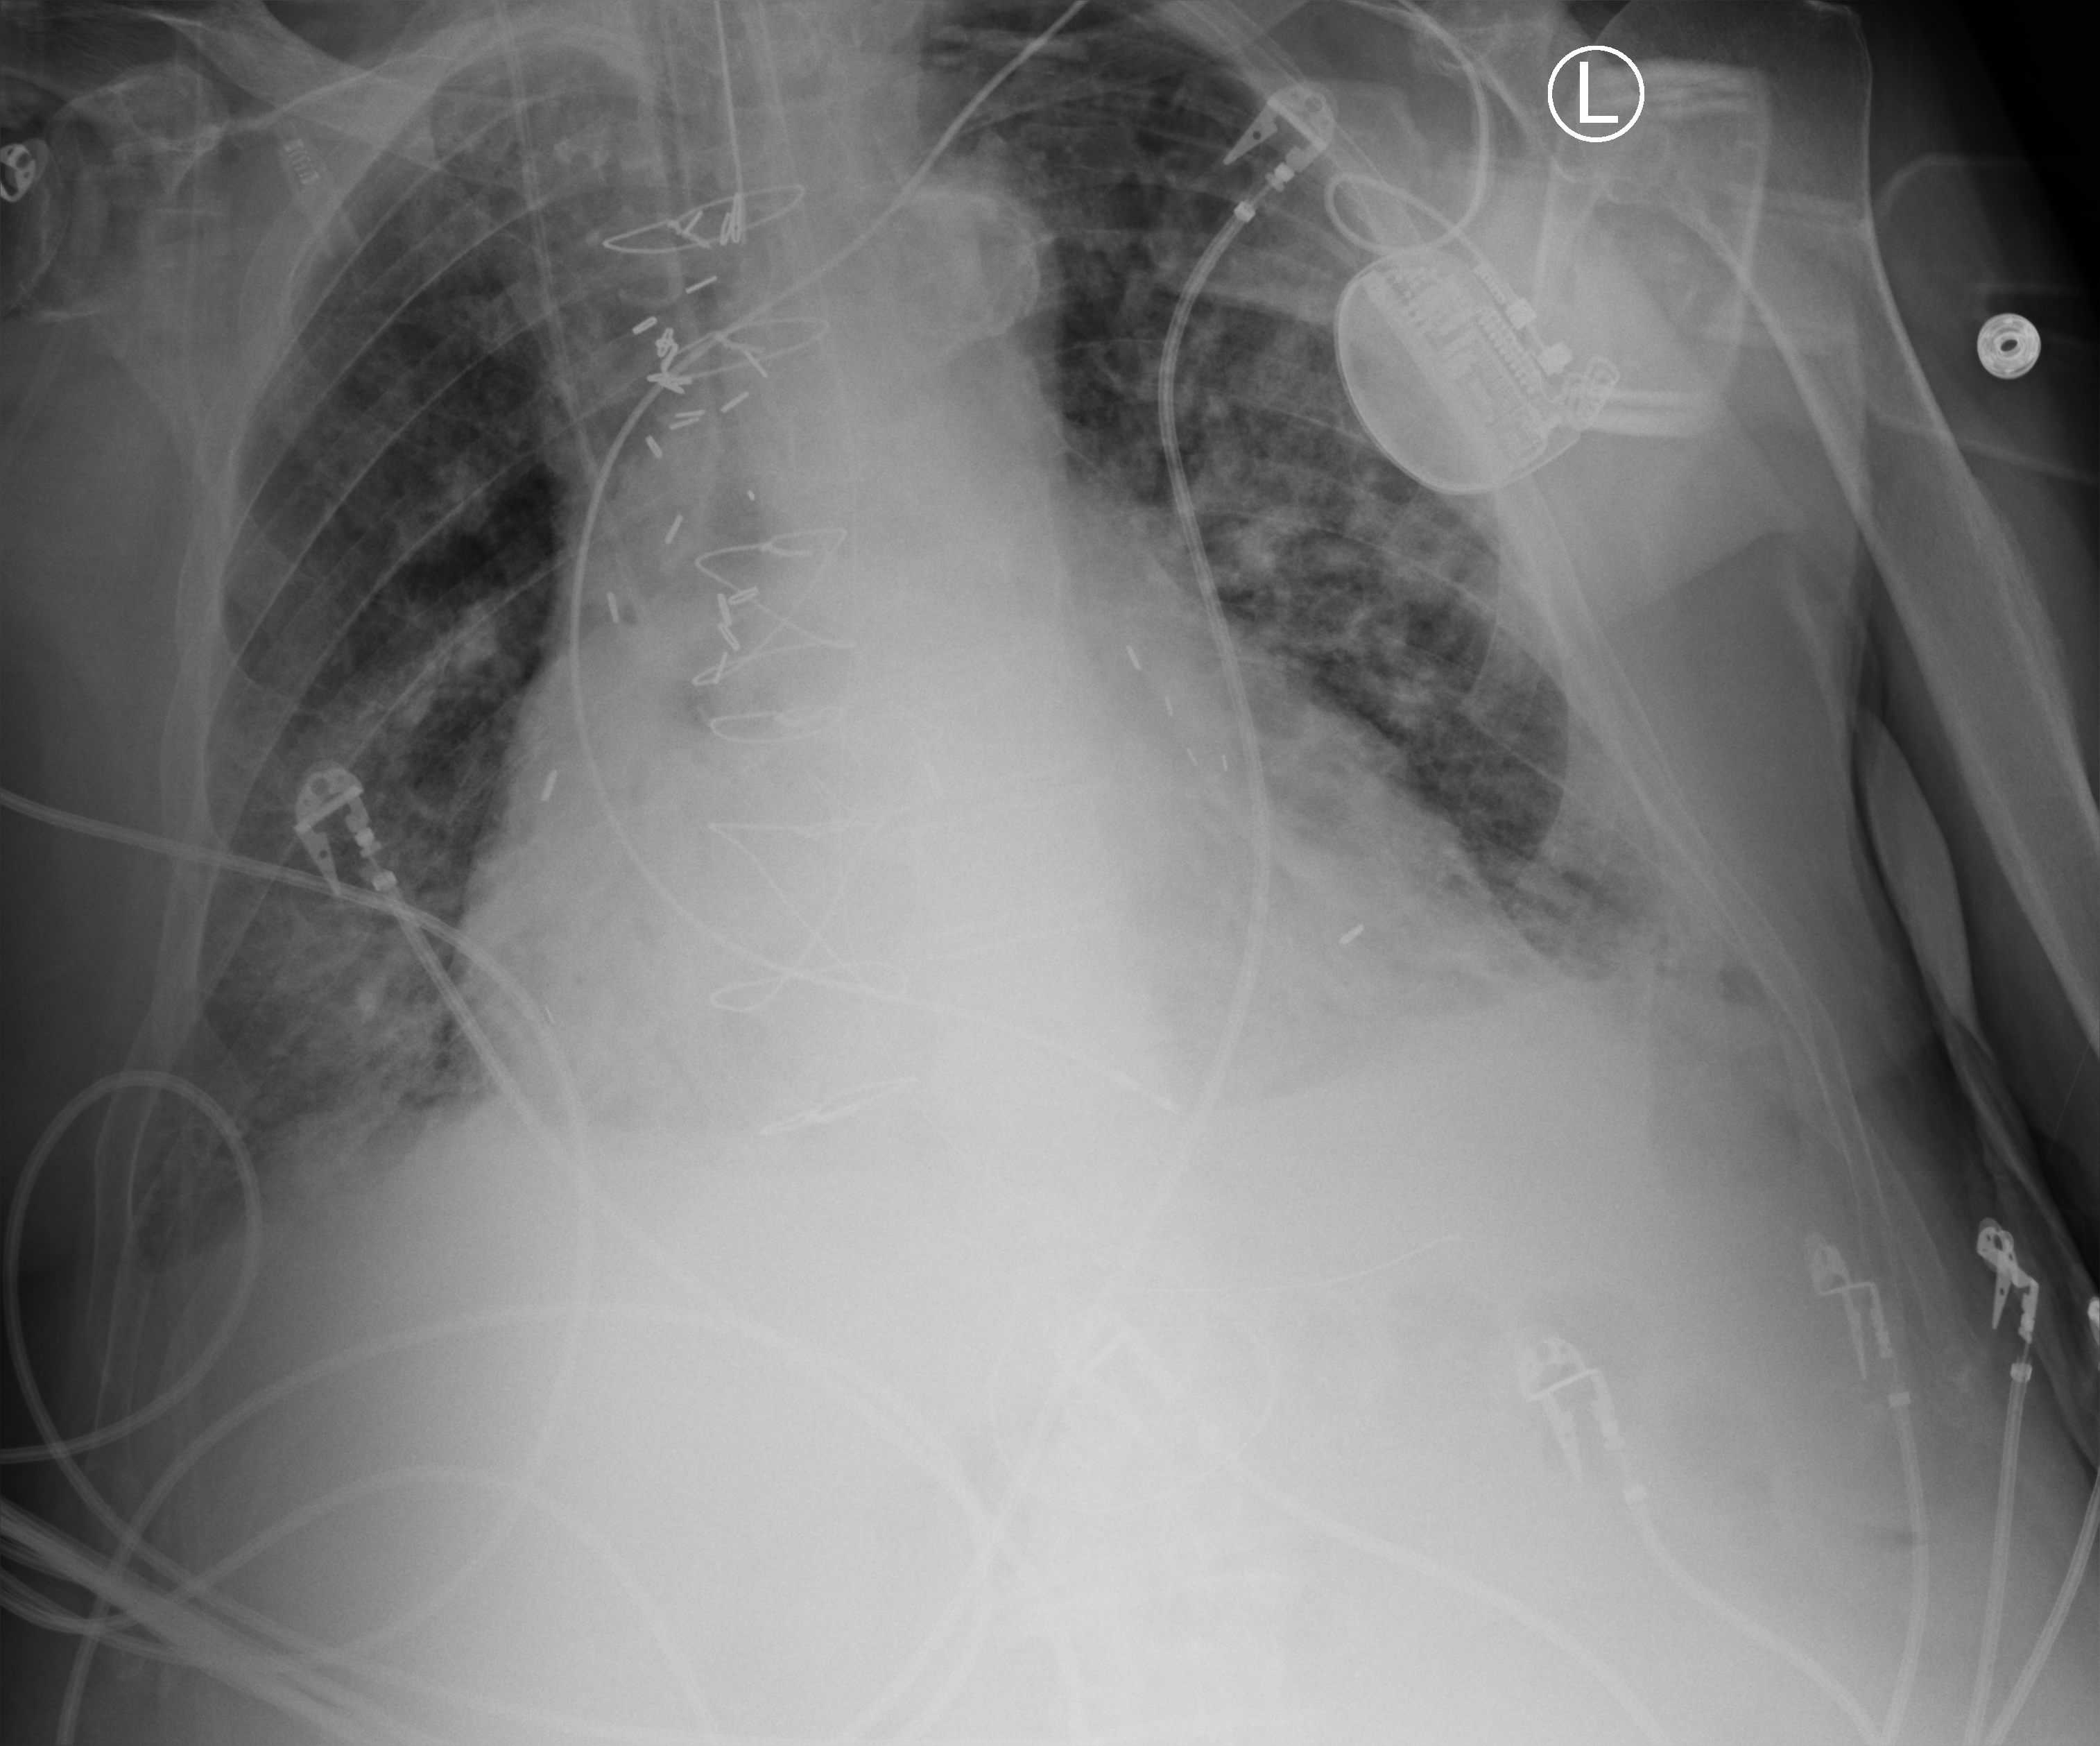
Portable chest radiograph; anteroposterior (AP) projection. Male patient hospitalised with COVID-19, age 75–90 years.
From the hospital-stay record, not from the radiograph (when in the stay this image was taken is not recorded): length of hospital stay: 16 days.